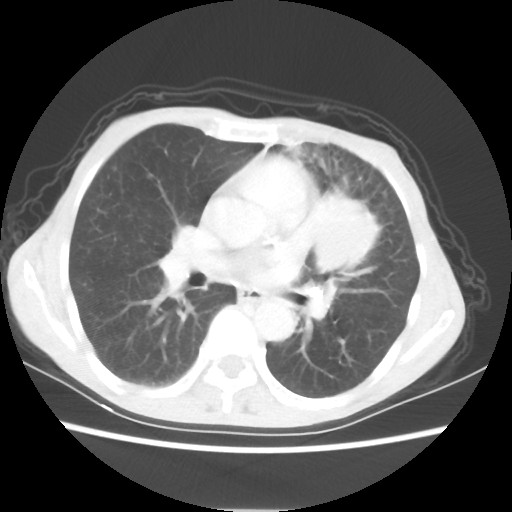
Chest CT, one axial slice. Position 32 of 56 along the scan axis. Reconstruction kernel STANDARD. Lung window (W 1500 / L -600 HU). 5 mm slice thickness. 512 × 512 image matrix, field of view 331 × 331 mm. Female patient, age 60 years. Case-level facts recorded for this patient, not image findings: clinical TNM (as recorded): T4 N1 M0.
Annotated regions visible in this slice (rectangle marked by the reading radiologist):
- lung tumour (recorded histology: adenocarcinoma): bounding box (x1, y1, x2, y2) in pixels: (307, 191, 381, 277)